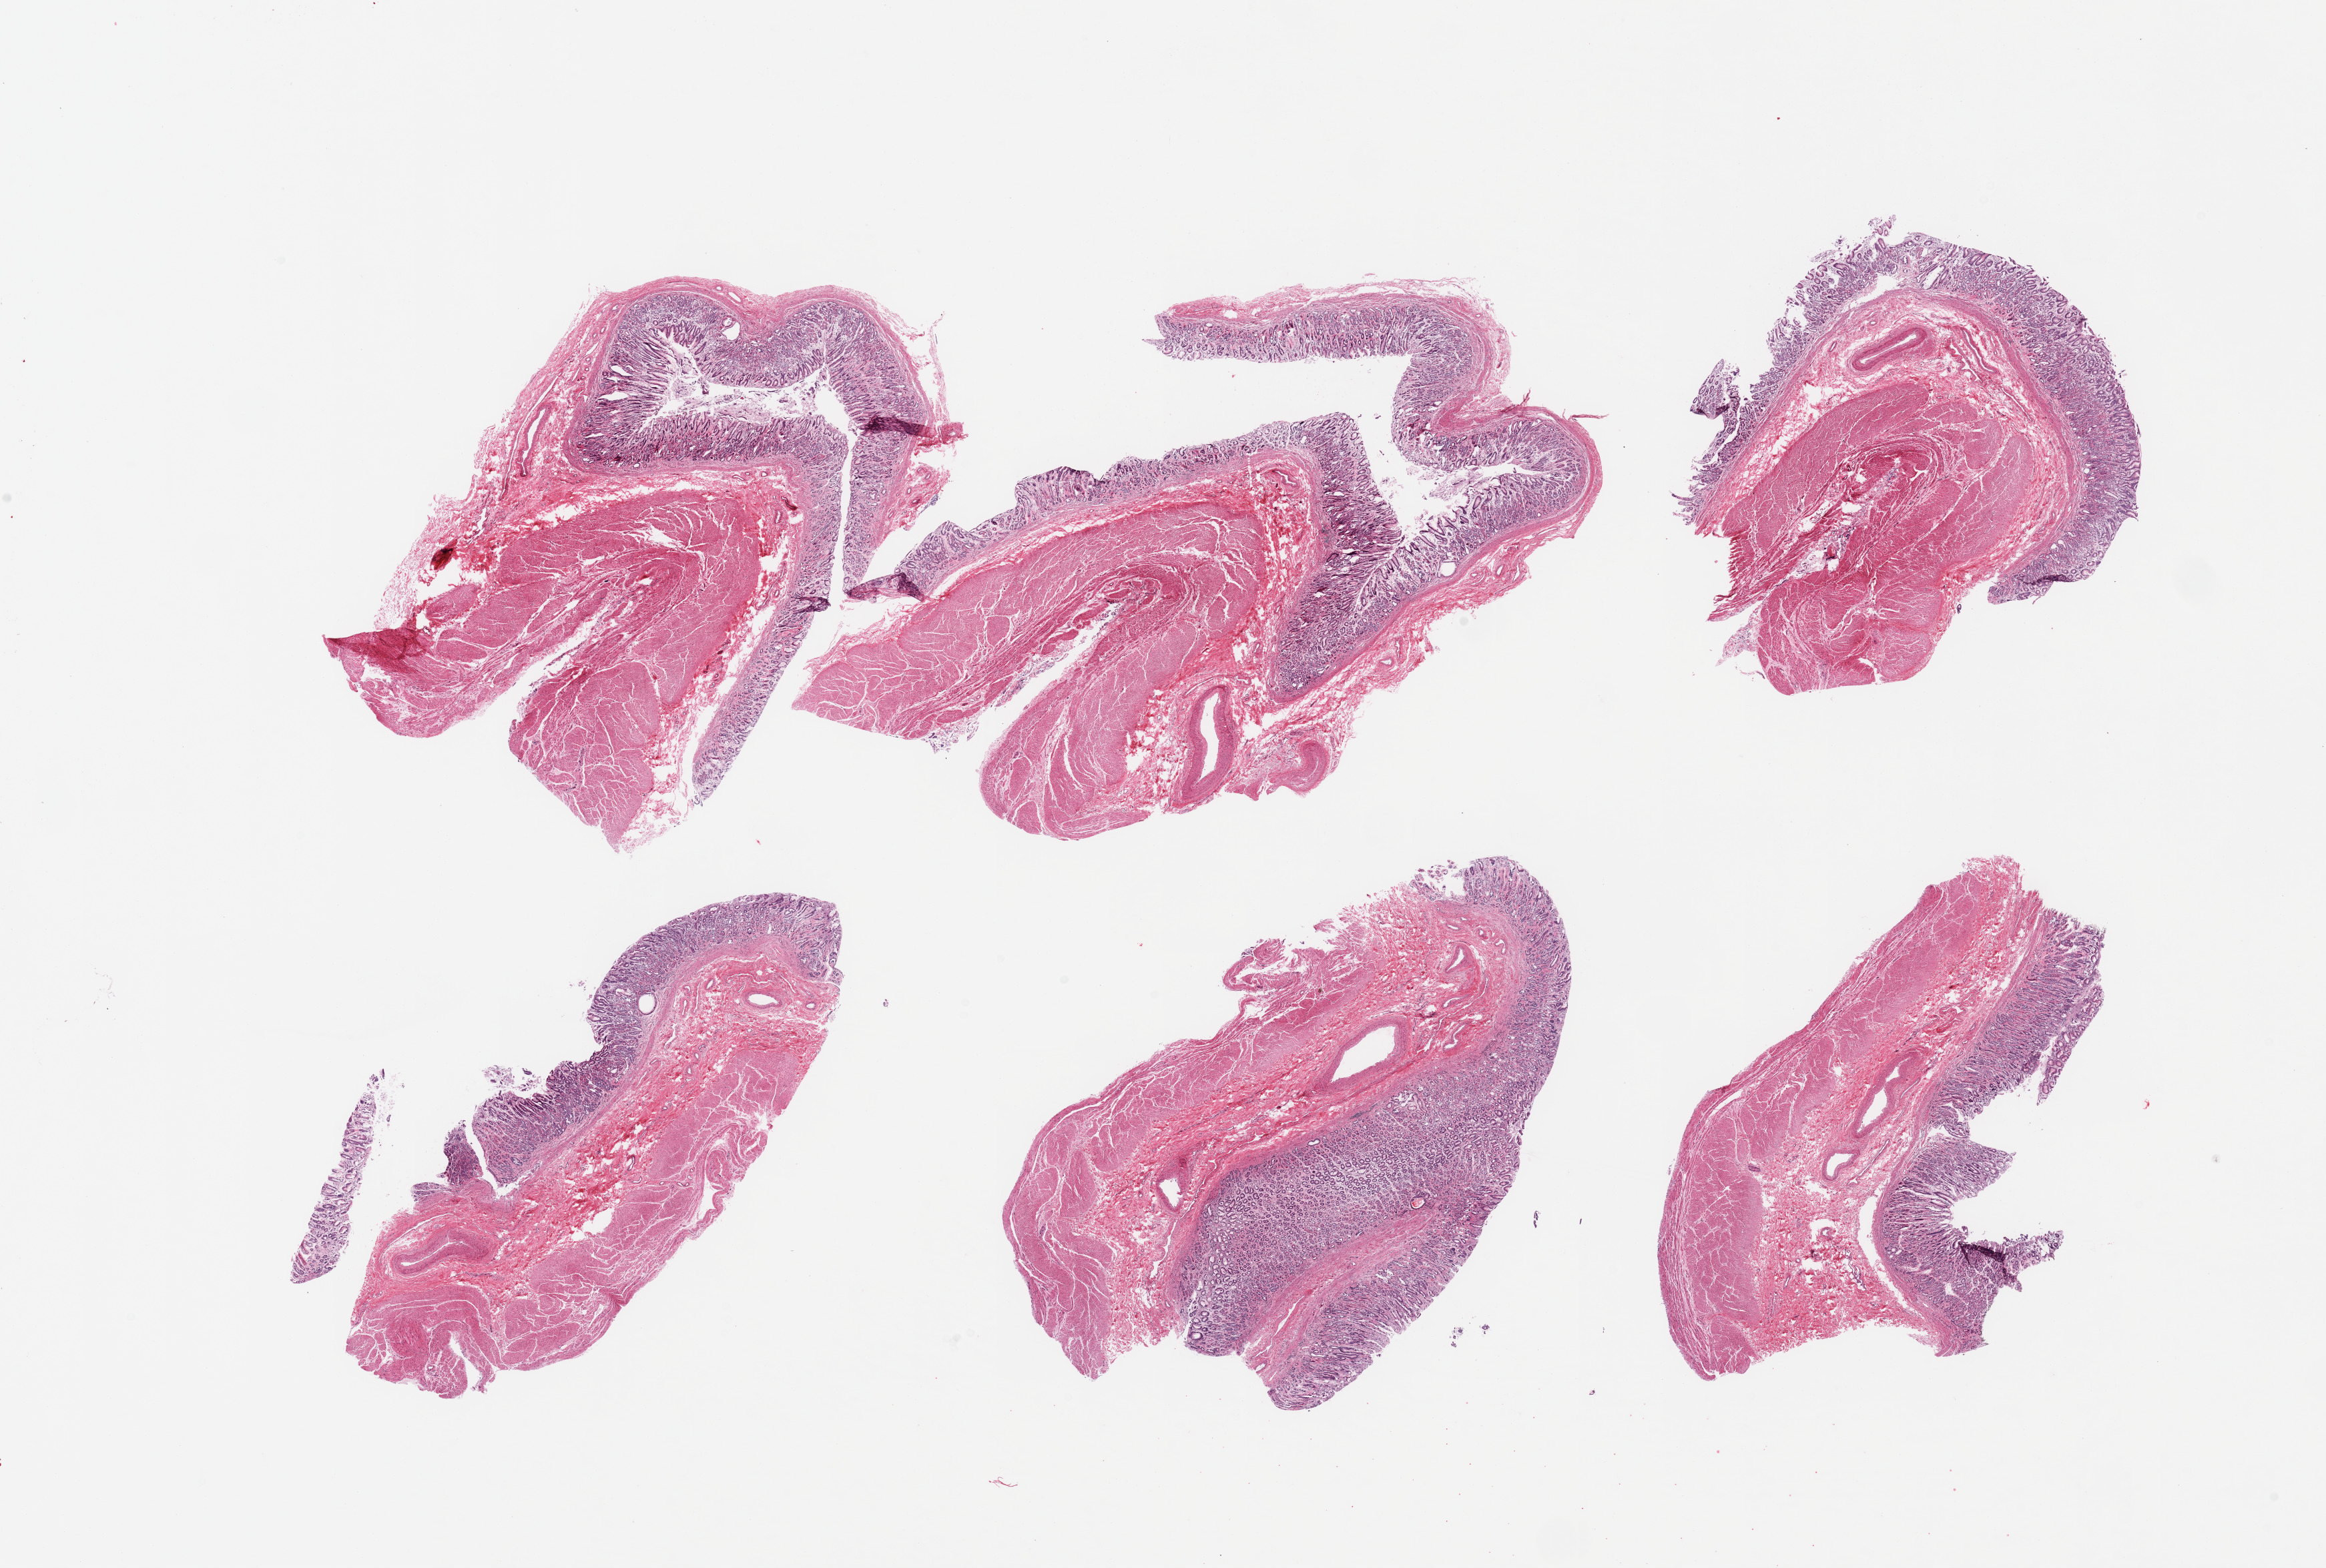
Hematoxylin and eosin (H&E) whole-slide image — low-resolution overview of the scanned area, about 27.6 x 18.6 mm. PAXgene-fixed, paraffin-embedded tissue. Section of stomach (target tissue). Tissue donor sample. Male donor.
Pathologist's review note for this sample: 6 pieces, approaches score 2 in pfoci; mucosa up to ~0.7mm, ~25-30% thickness.